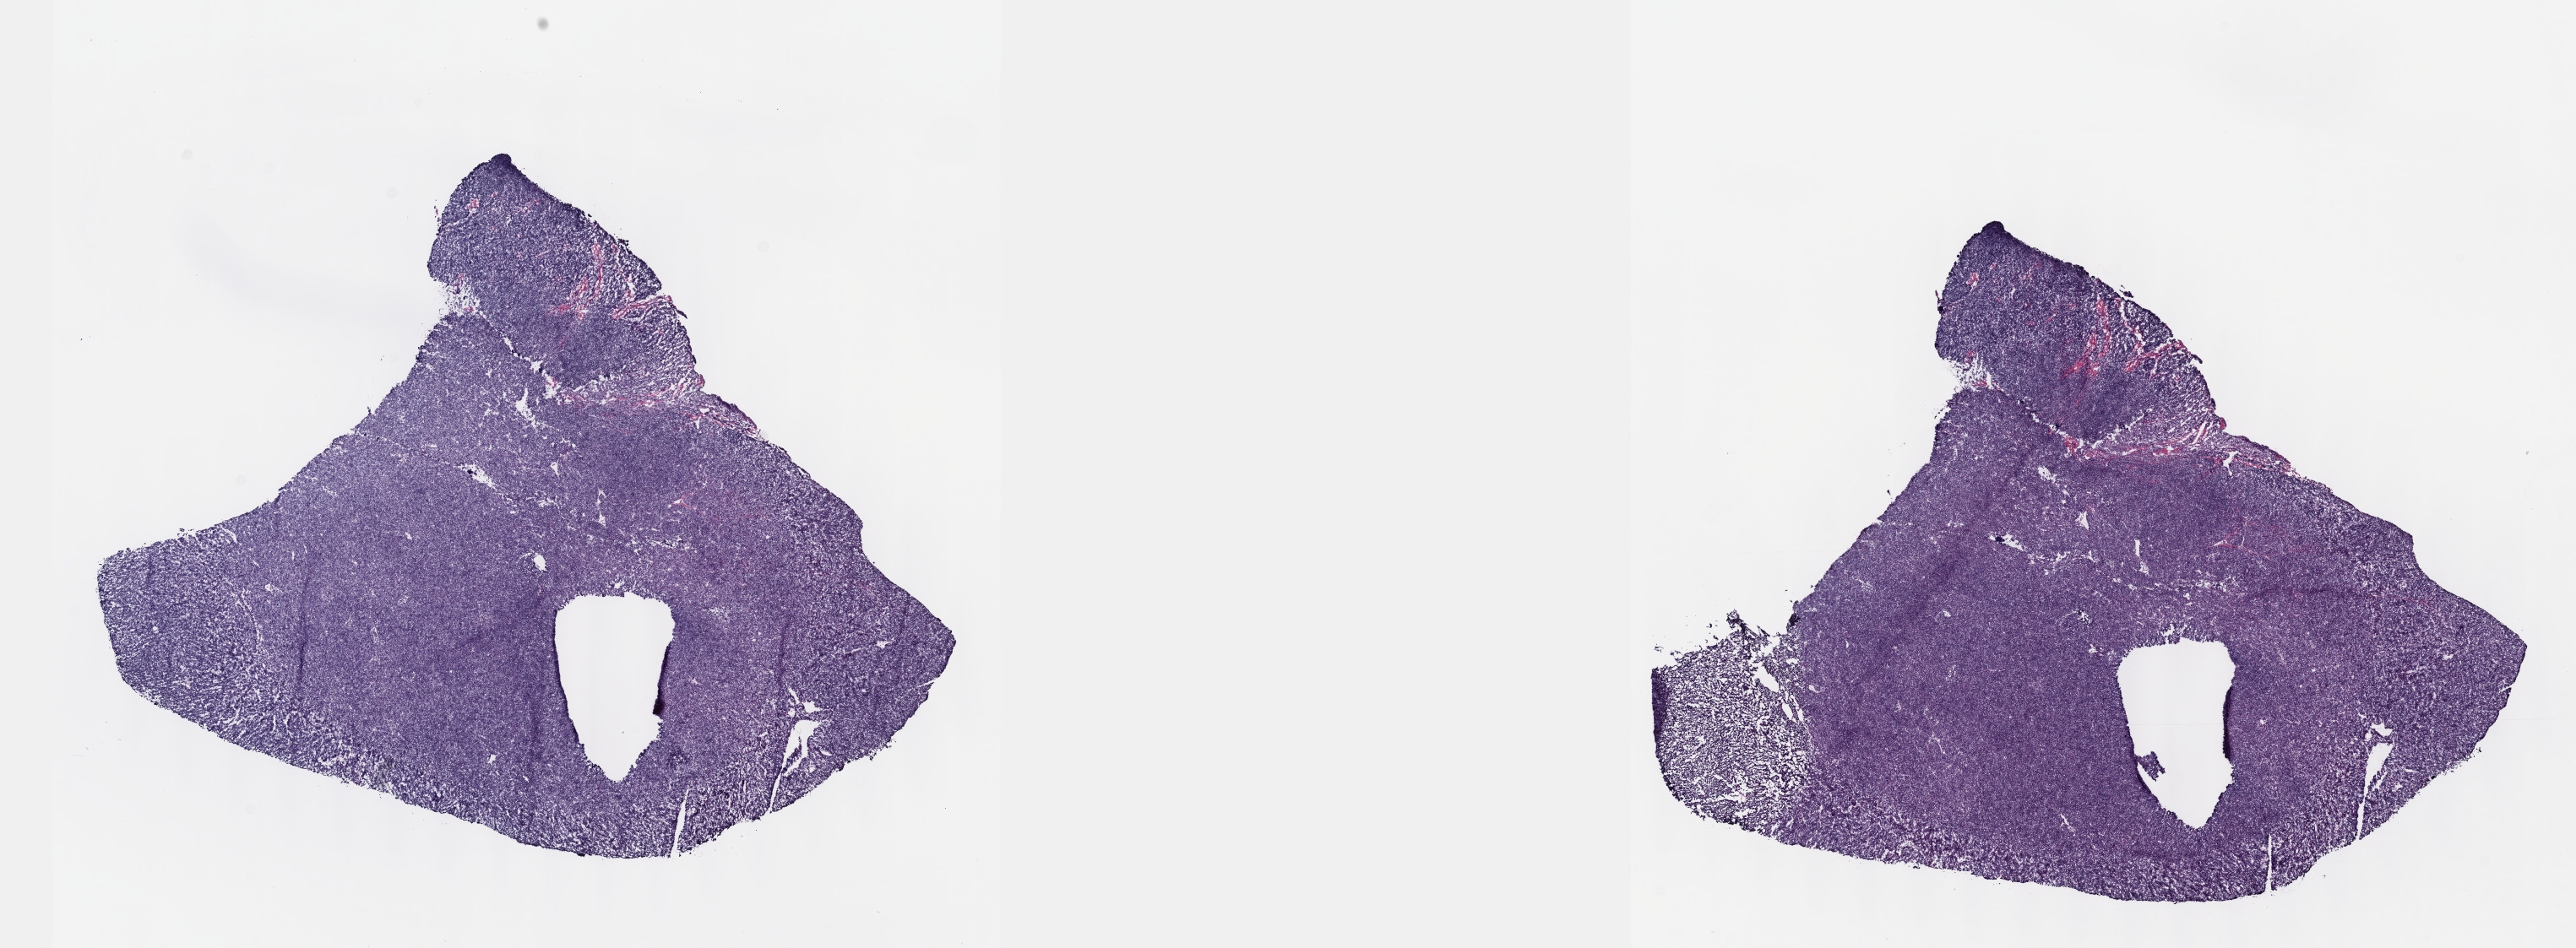
Digitized Hematoxylin and eosin (H&E) stained tissue section (whole slide) — whole scanned area (about 24.6 x 9.1 mm, acquisition: 40x scan) shown as a low-resolution overview, frozen section from the top of the tissue portion, thymus, primary tumour sample. Female patient; age at initial diagnosis 74 years. Composition of this section per pathologist review: tumour cells 99%, tumour nuclei 99%, normal cells 0%, stromal cells 1%, necrosis 0%. Infiltration values recorded for this section: lymphocyte infiltration 0%, monocyte infiltration 0%, neutrophil infiltration 0%.
Pathologic diagnosis: Thymoma, type AB, malignant (anterior mediastinum).